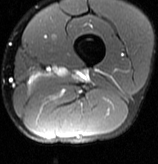
MRI of an extremity soft-tissue mass, one axial slice; slice 14 of 70 in the series (ordered by position); T2-weighted fat-saturated; MR volume resampled by the dataset authors to the PET/CT grid (not the native acquisition matrix); 158 × 164 image matrix, field of view 154 × 160 mm. Male patient. From the clinical record (not read from this slice): histological type: extraskeletal osteosarcoma; grade: high; site of the primary tumour: left adductur.
Structures marked on this image (expert contour drawn on MRI and transferred to this co-registered scan by the dataset authors):
- gross tumour volume (mass): box from (x=72, y=69) to (x=89, y=81) px